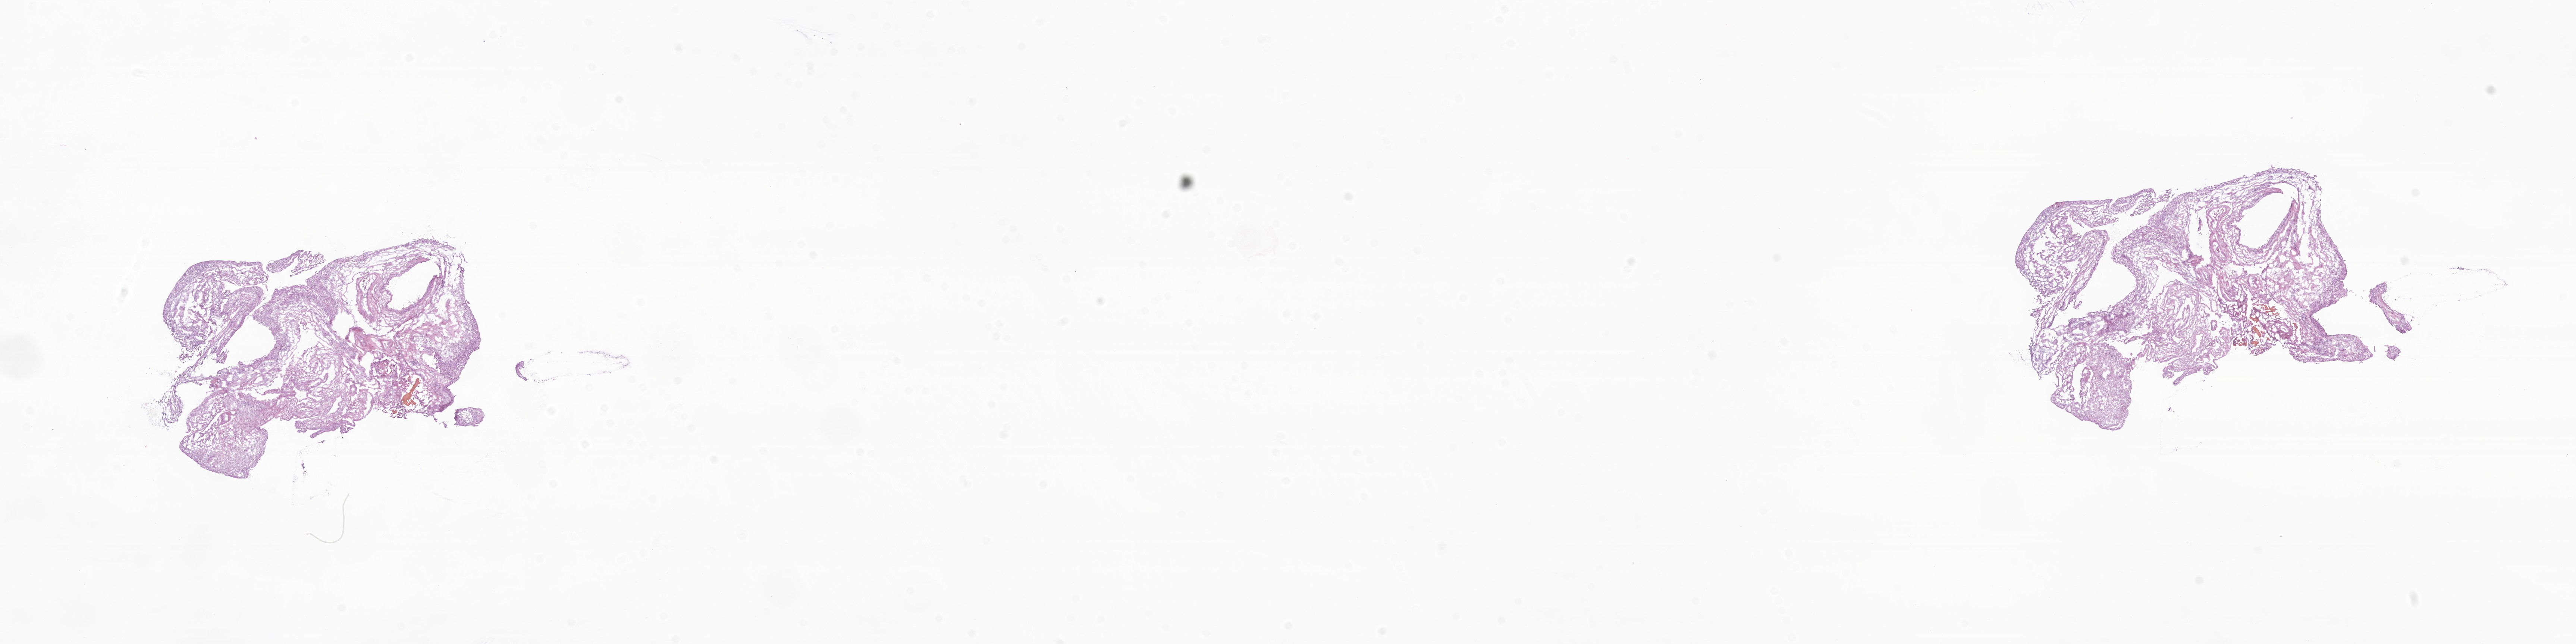
Hematoxylin and eosin (H&E) whole-slide image of tumor tissue from the brain — whole scanned area (about 29.1 x 7.3 mm) shown as a low-resolution overview. Frozen section. Patient: female, age 53 months (4 years 5 months).
Recorded diagnosis: Craniopharyngioma, adamantinomatous.